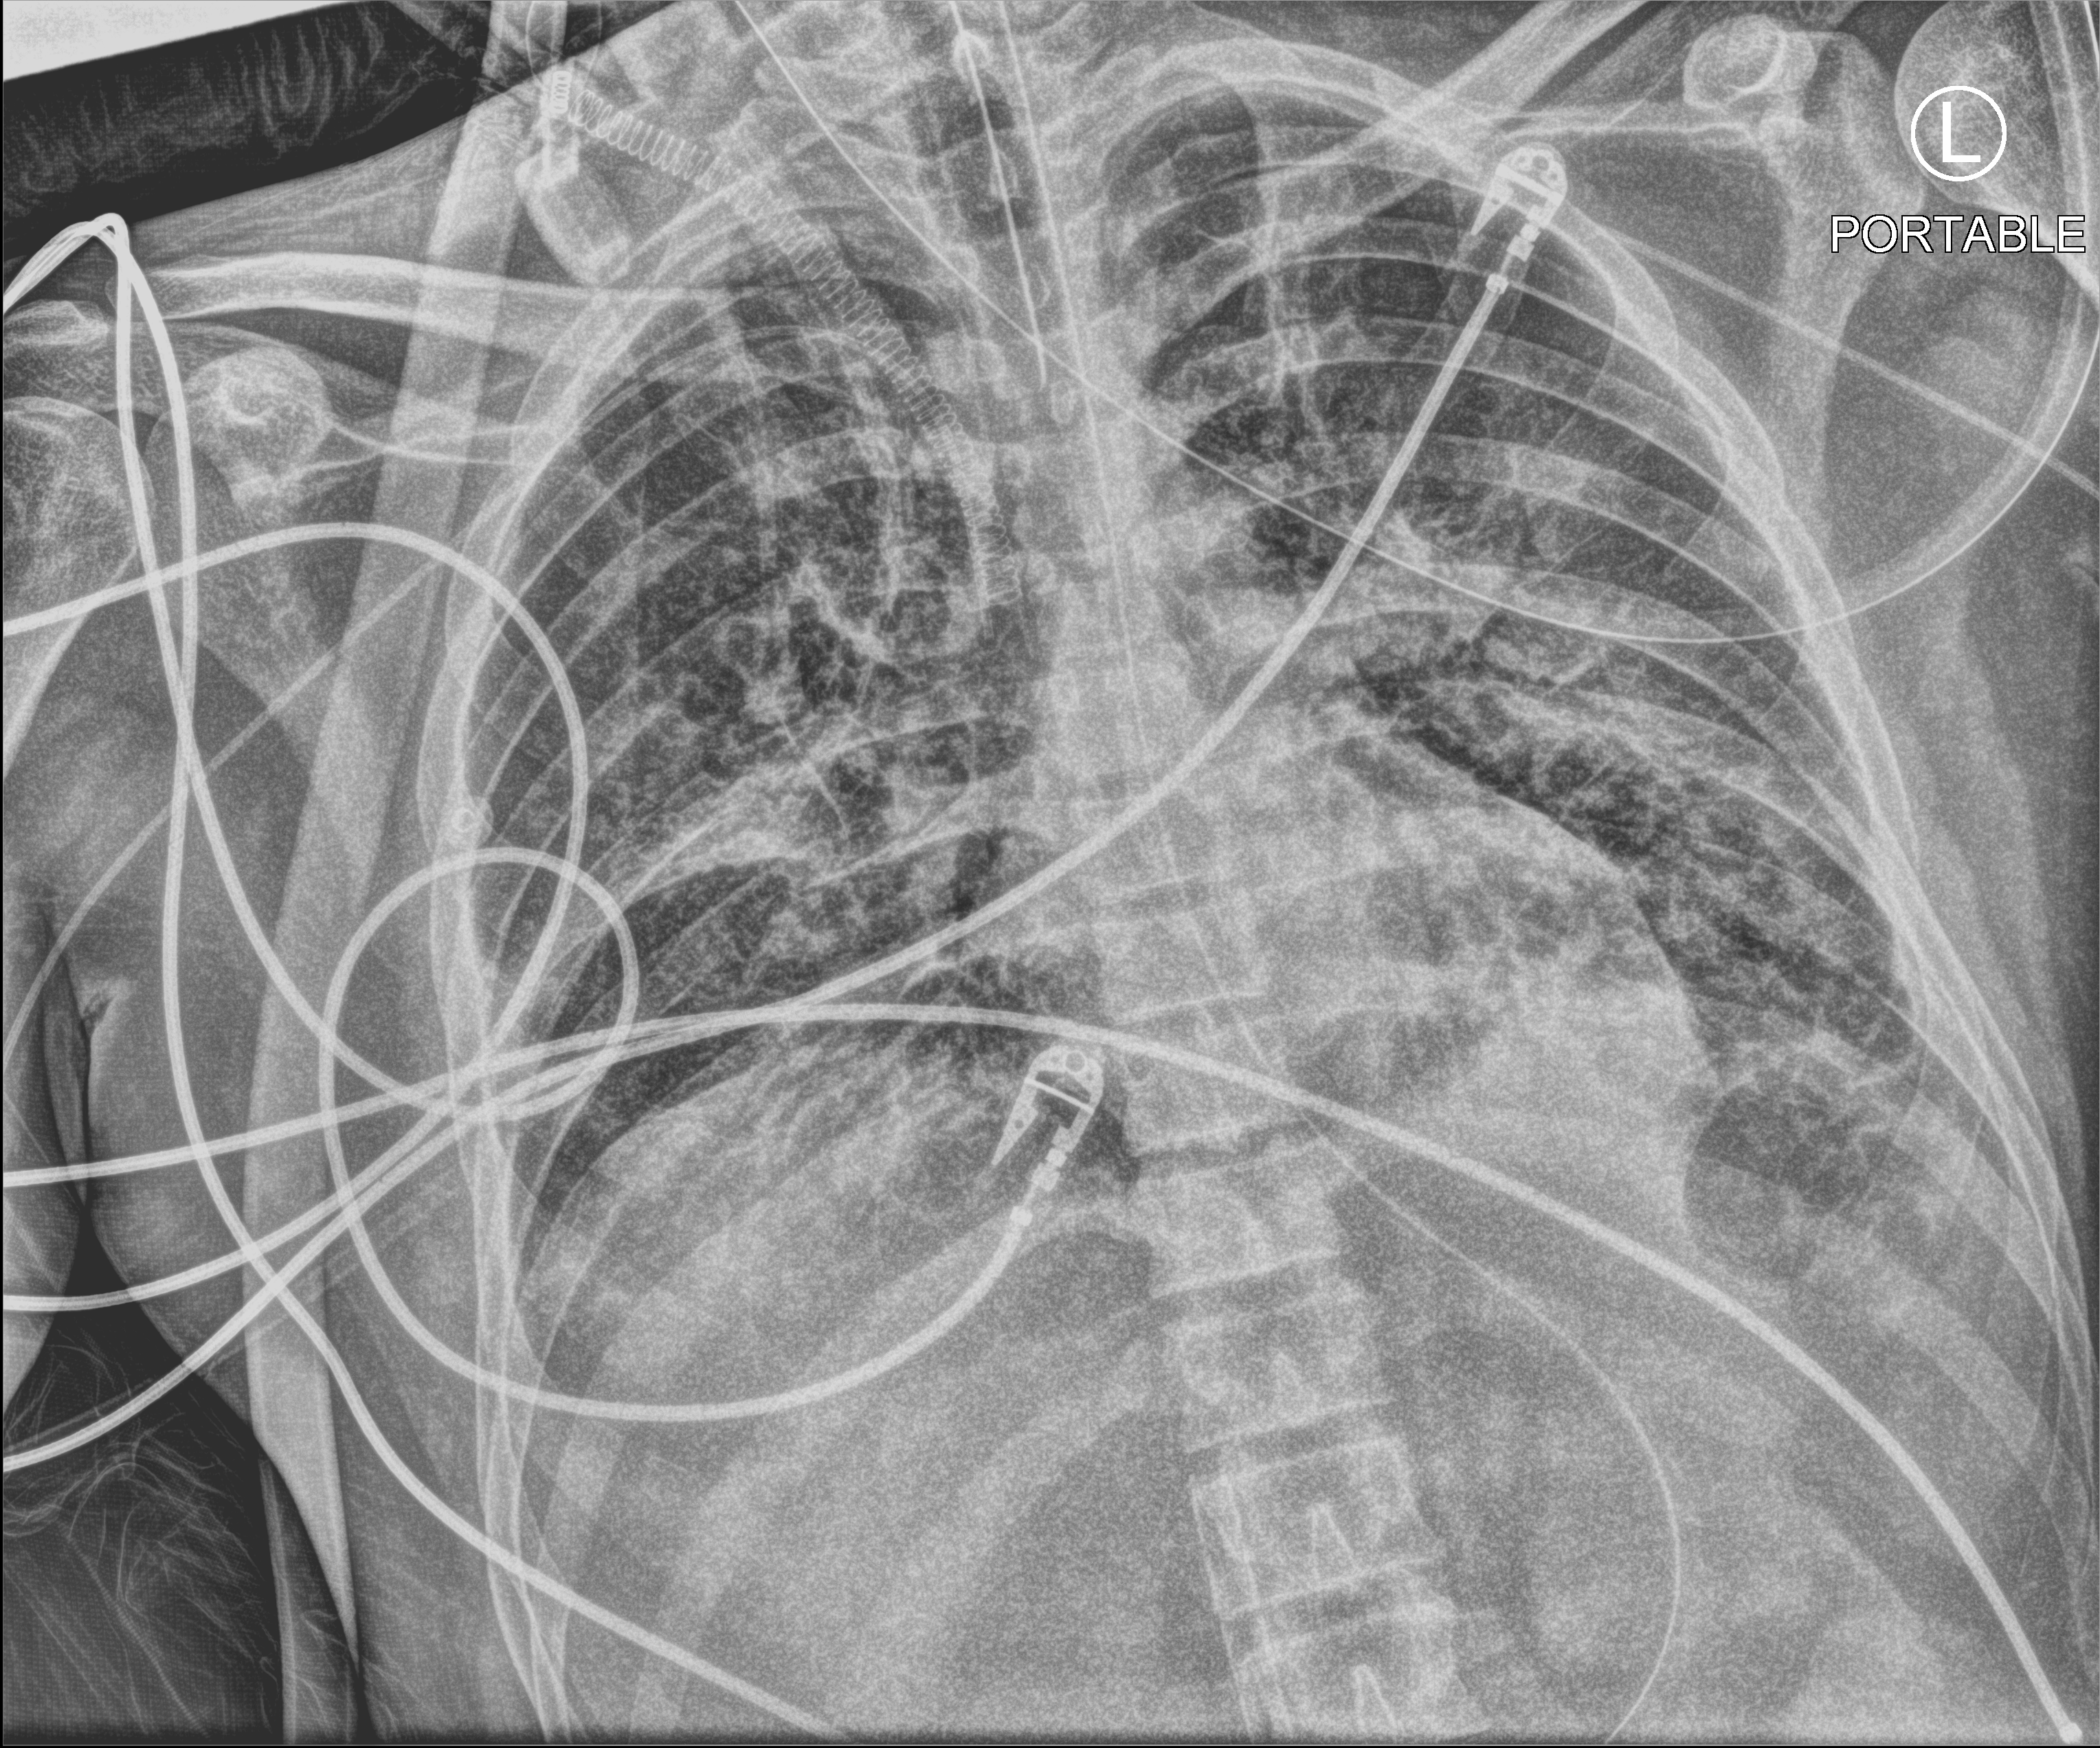
Bedside chest radiograph (computed radiography). Adult patient hospitalised with COVID-19, age 18–59 years.
Hospital-stay facts (about this admission, not read from this image; timing relative to this image not recorded):
- mechanically ventilated during this hospital stay: yes
- admitted to intensive care during this hospital stay: yes